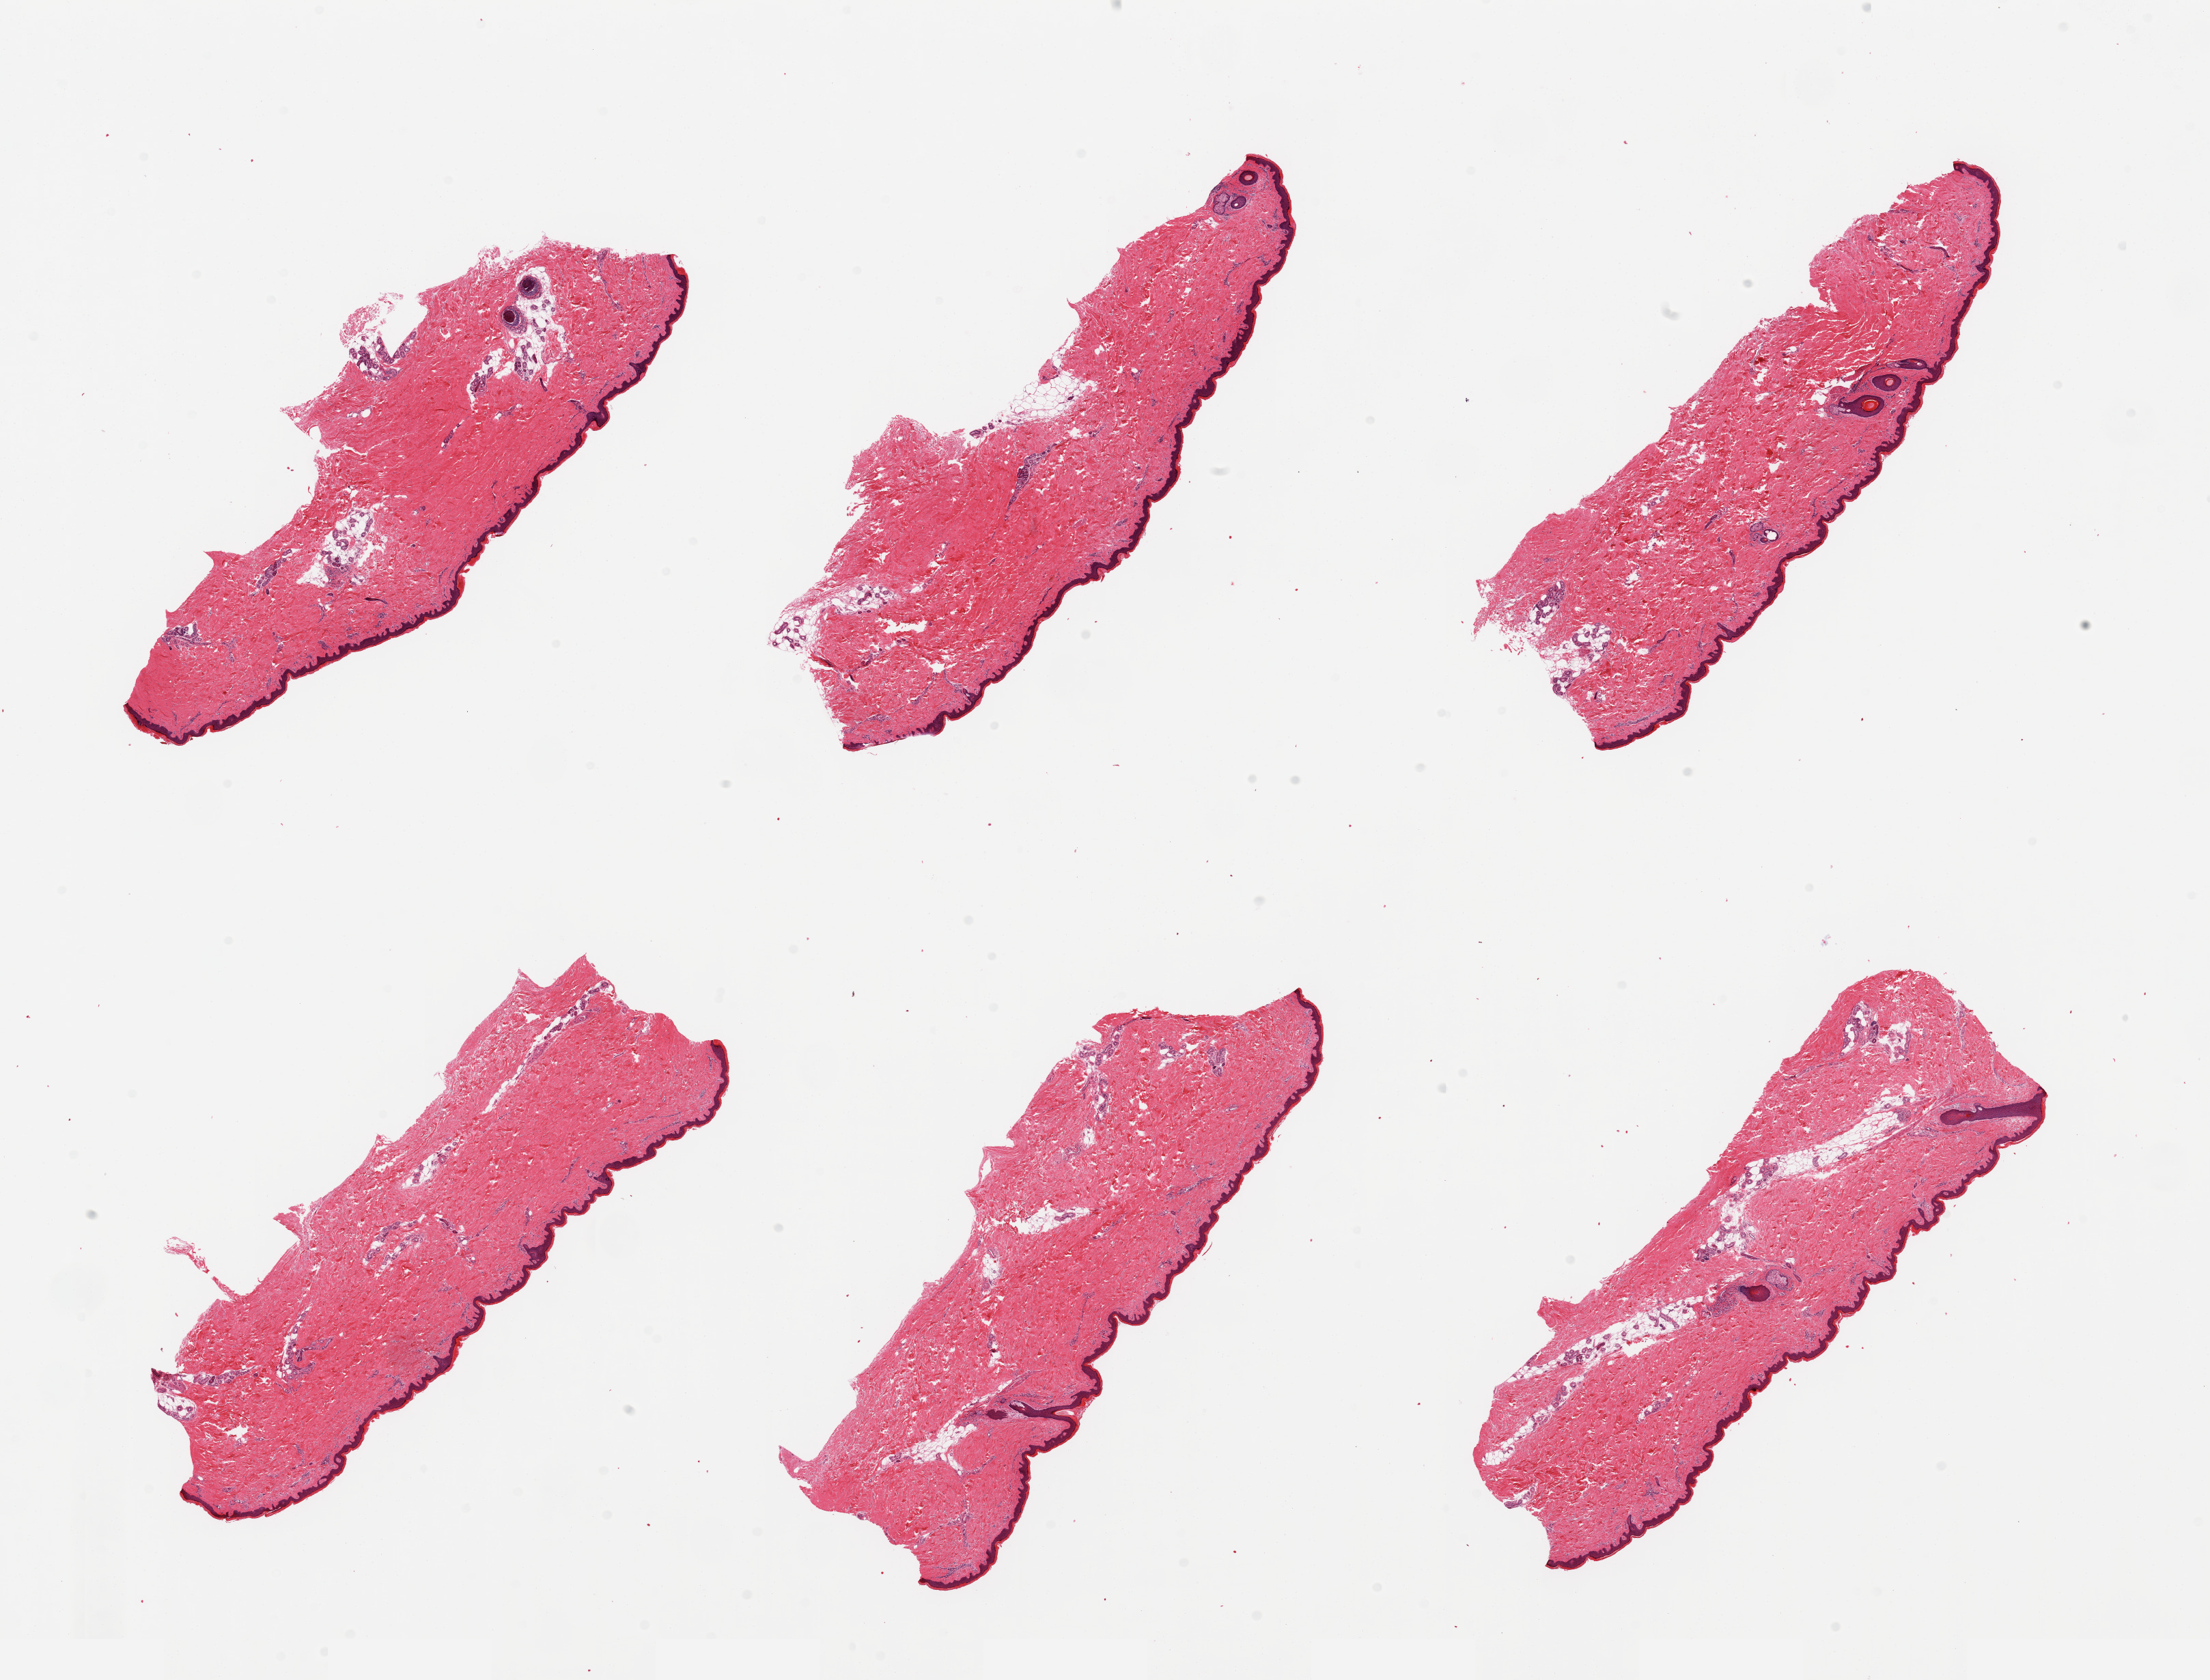
Digitized H&E-stained section, brightfield — a low-resolution overview of the entire scanned area, about 25.6 x 19.5 mm; PAXgene-fixed, paraffin-embedded tissue; target tissue: skin of lower leg; donor tissue sample.
Reviewer comment on this tissue sample: 6 pieces; well trimmed; 5-10% dermal fat.